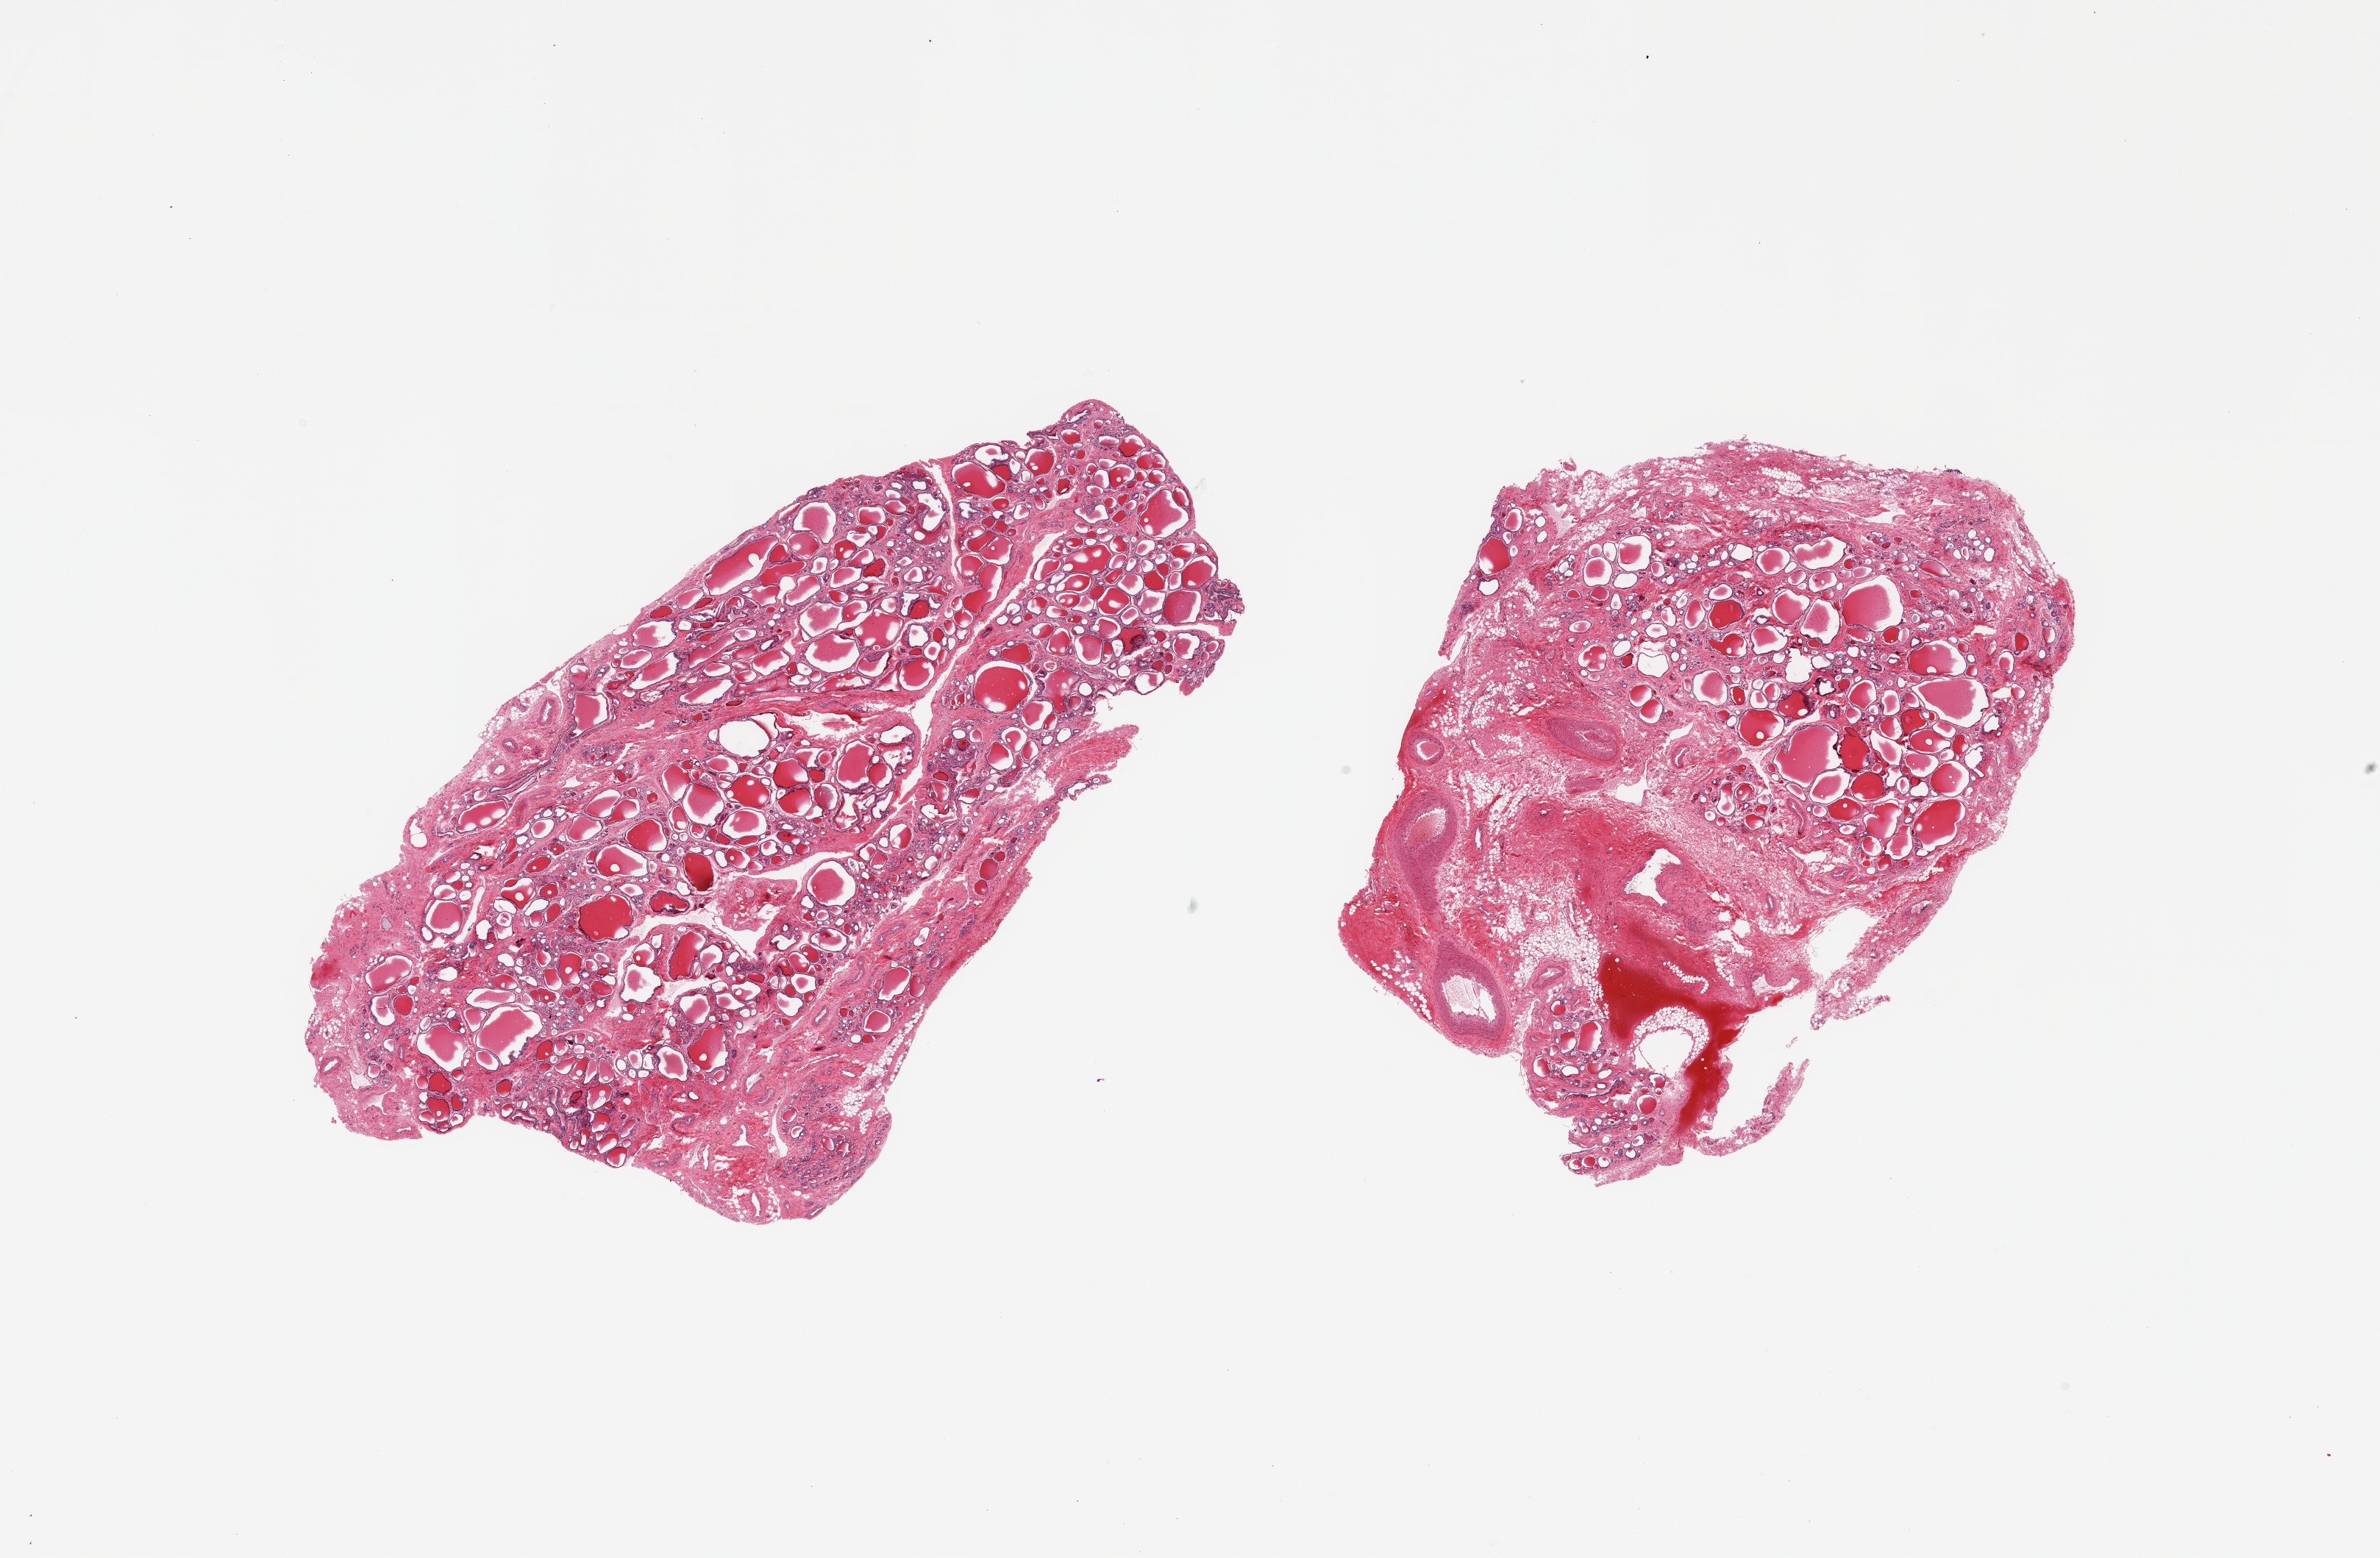
Whole-slide image, H&E stain — shown as a low-resolution overview of the whole scanned area (about 25.6 x 16.8 mm); PAXgene-fixed, paraffin-embedded tissue; section of thyroid (target tissue); donor tissue sample. Donor: male.
Review note (as recorded): 2 pieces; 1 piece contains 60% fibrovascular stroma.